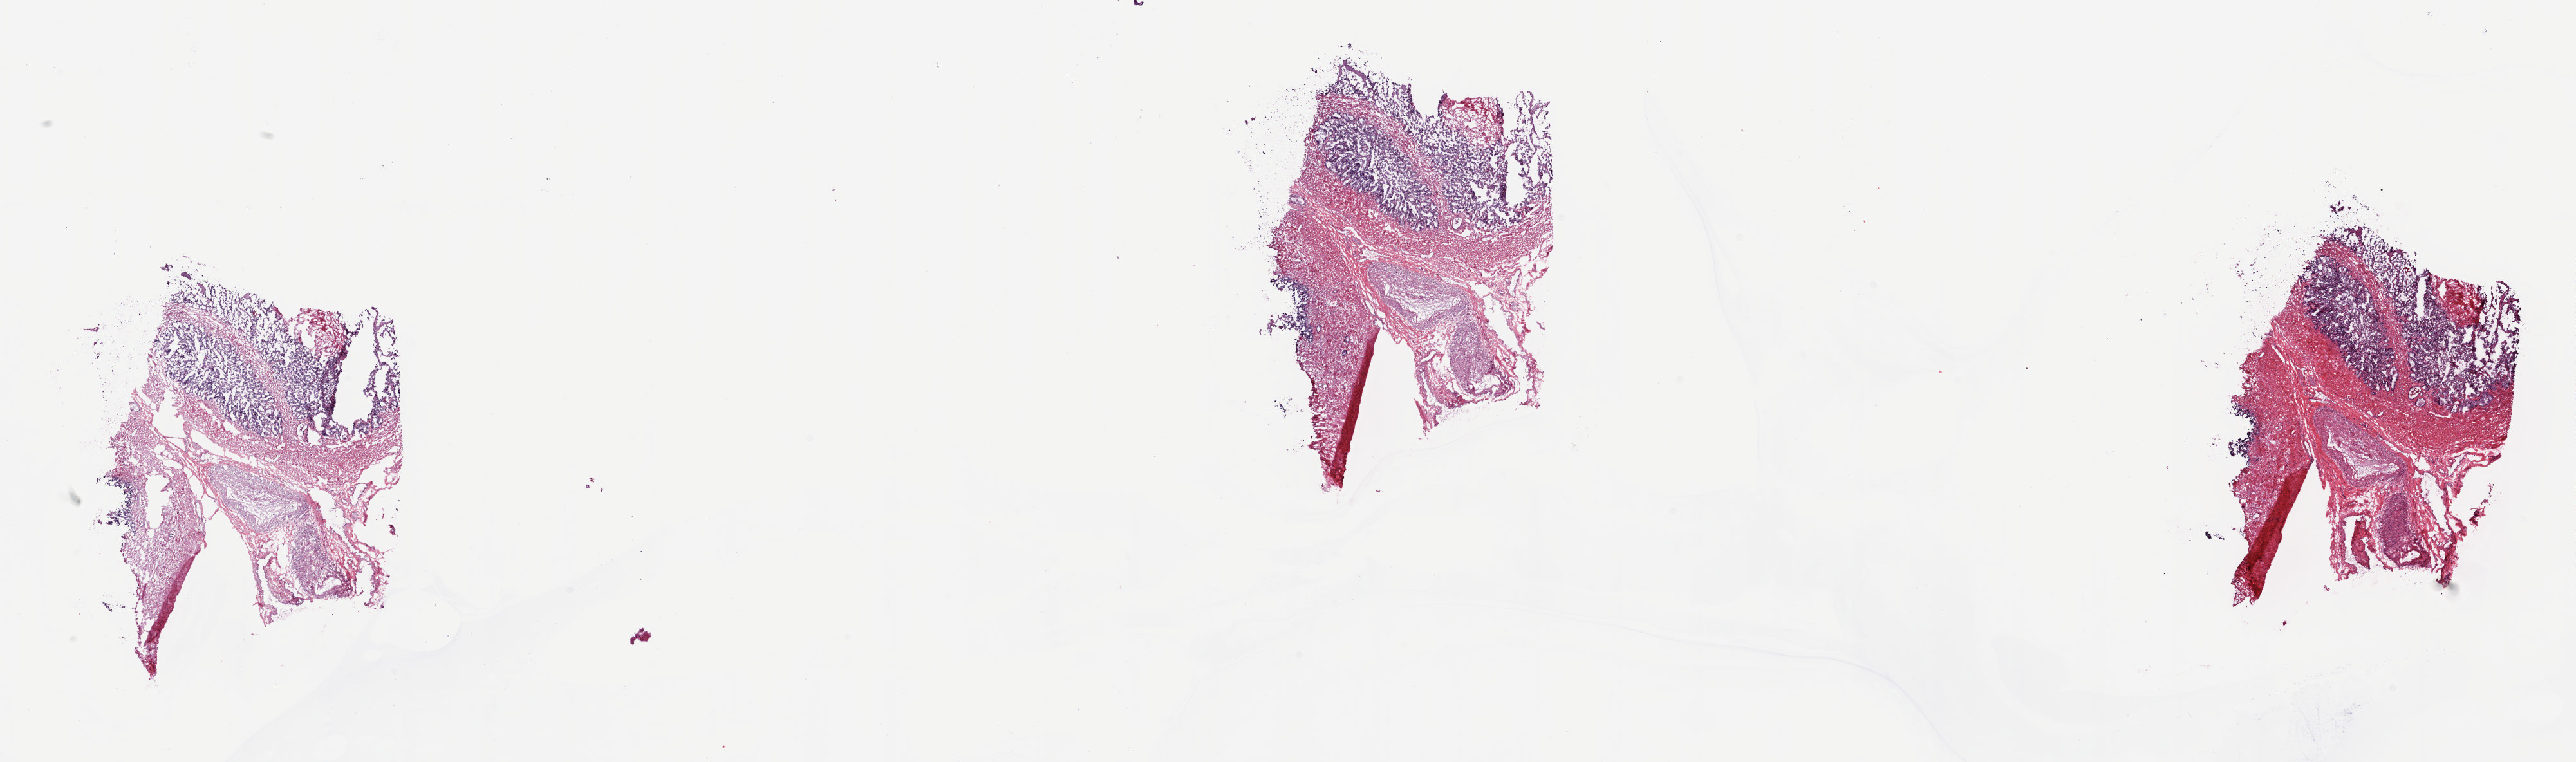
Whole-slide histology image, Hematoxylin and eosin (H&E) stained, low-resolution overview of the scanned area, about 31.7 x 9.4 mm (from a 20x scan); frozen section from the top of the tissue portion; sample: solid tissue normal (non-tumour tissue), prostate. Male patient; age at initial diagnosis 56 years. Composition of this section per pathologist review: tumour cells 0%, tumour nuclei 0%, normal cells 40%, stromal cells 60%, necrosis 0%. Infiltration values recorded for this section: lymphocyte infiltration 70%, monocyte infiltration 10%, neutrophil infiltration 20%.
This section: solid tissue normal sample (biorepository sample class). Patient diagnosis: Adenocarcinoma, NOS (prostate gland).